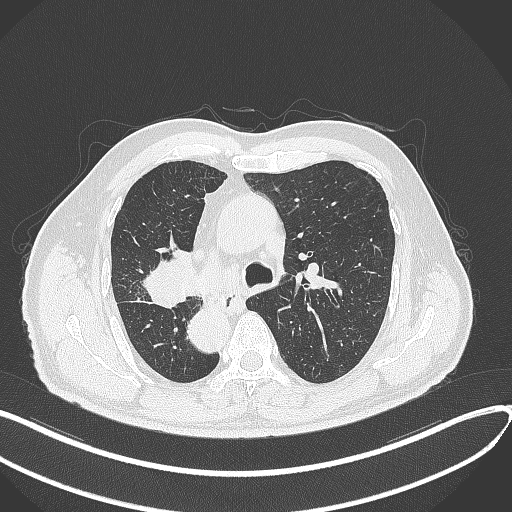
Chest CT, one axial slice. Slice 205 of 300 in the series (ordered by position). 120 kVp. Lung window (W 1500 / L -600 HU). 512 × 512 image matrix. Male patient, age 67 years. Case-level facts recorded for this patient, not image findings: clinical TNM (as recorded): T2a N0 M0.
Annotated regions visible in this slice (rectangle marked by the reading radiologist):
- lung tumour (recorded histology: squamous cell carcinoma): bounding box <140,244,197,309> (left, top, right, bottom; pixels)